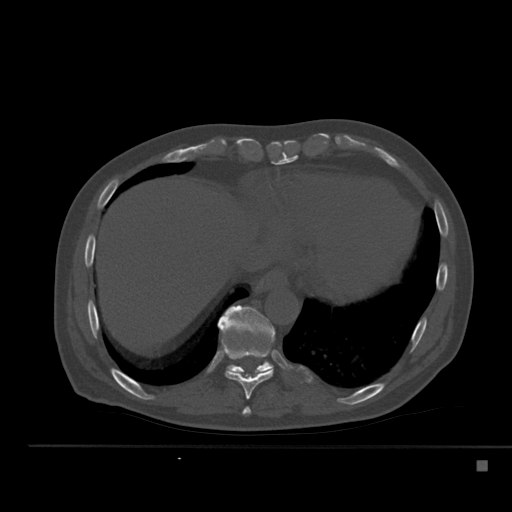
CT including the spine, one axial slice. Position 282 of 517 along the scan axis. Bone window (W 1800 / L 400 HU). 1.5 mm slice thickness. 512 × 512 image matrix, field of view 408 × 408 mm. Patient: male, 70 years. From the clinical record (not read from this slice): primary cancer: renal; vertebrae with lytic lesions (as recorded): T4, T6, T10, T12, L3, L4, L5.
Outlined on this slice (semi-automatic segmentation, software-assisted and operator-edited):
- T10 vertebra: box from (x=218, y=305) to (x=275, y=375) px
- T8 vertebra: (x=242, y=407)–(x=251, y=415)
- T9 vertebra: (x=220, y=338)–(x=273, y=400)